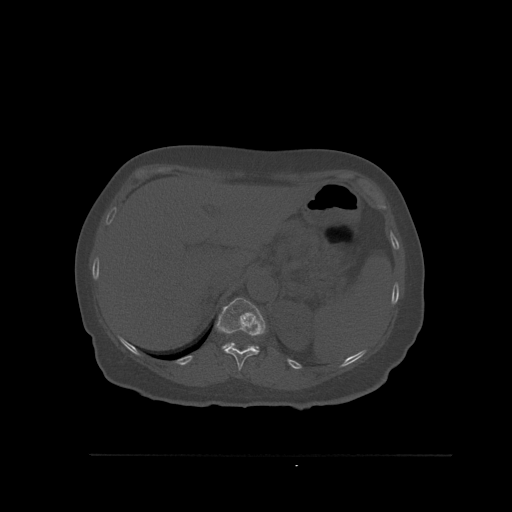
CT including the spine, one axial slice; position 296 of 527 along the scan axis; bone window (W 1800 / L 400 HU); 512 × 512 image matrix, field of view 470 × 470 mm. Female patient, age 73 years. Case-level facts recorded for this patient, not image findings: primary cancer: breast.
Outlined on this slice (semi-automatically segmented with operator editing):
- T11 vertebra: bounding box <223,347,259,371> (left, top, right, bottom; pixels)
- T12 vertebra: <215,298,266,351>